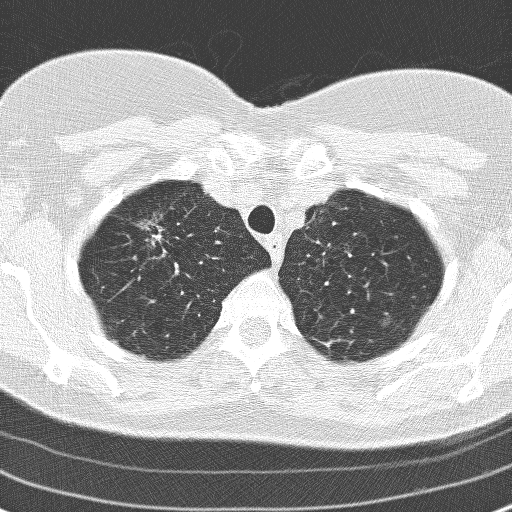
Chest CT (low-dose screening protocol), one axial image, second screening round (one year after baseline), lung window (W 1500 / L -600 HU), lung (sharp) reconstruction kernel (D), slice 29 of 160 in the series, 512 × 512 image matrix. Female participant, aged 60 years at enrolment.
- Expert reader's lesion annotation, bounding box (x1, y1, x2, y2) in pixels: (126, 205, 181, 258).
- The exam's reader record, not a measurement of the box and not confirmed to be the same lesion: non-calcified nodule or mass ≥4 mm, right upper lobe, 17 × 15 mm, spiculated (stellate) margins, soft tissue attenuation, pre-existing on the prior screen: yes; interval growth: yes.
- Official screen result: positive, other.
- Later outcome: lung cancer diagnosed 78 days after this screen — adenocarcinoma, NOS, right upper lobe, moderately differentiated (G2), stage IA (AJCC 6th edition), 23 mm at pathology.